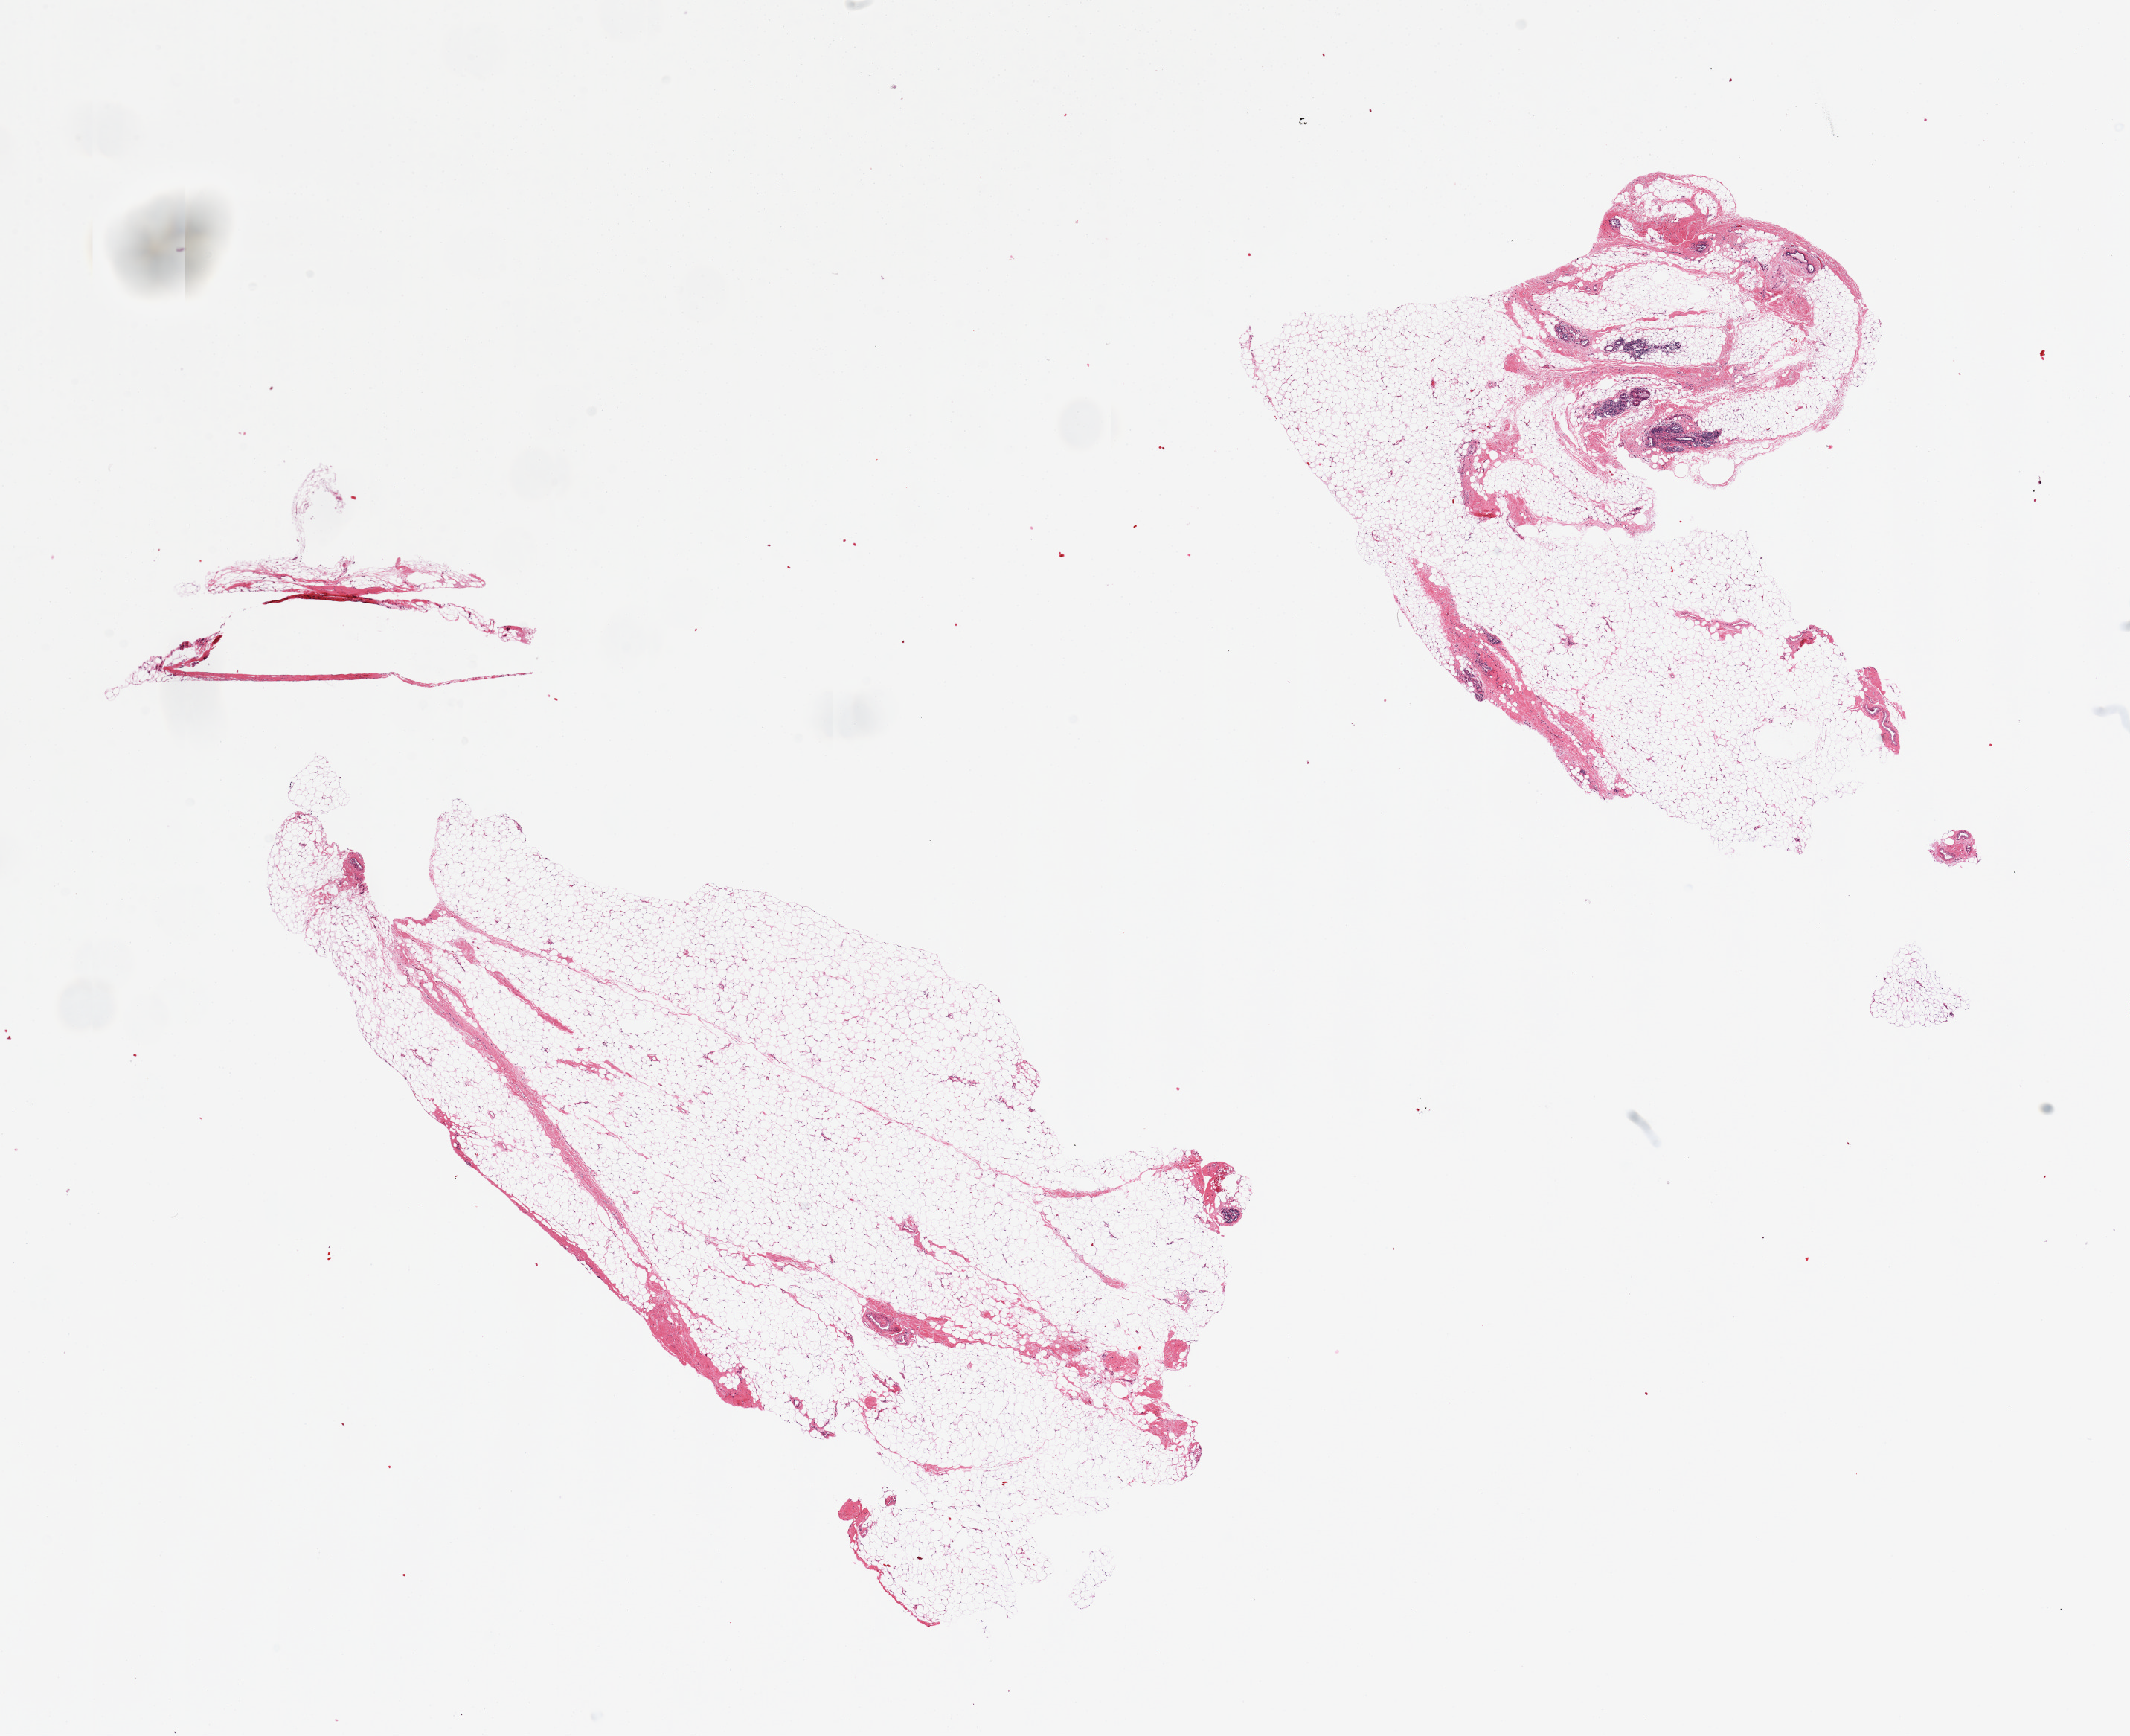
Whole-slide image, haematoxylin and eosin stain — shown as a low-resolution overview of the whole scanned area (about 22.6 x 18.5 mm, acquisition: 20x scan). PAXgene-fixed, paraffin-embedded tissue. Sampled site (target tissue): breast. Tissue donor sample. Donor: female.
* pathologist's review note for this sample: 2 pieces; largely fatty tissue with ductal-lobular units essentially confined to 1 piece